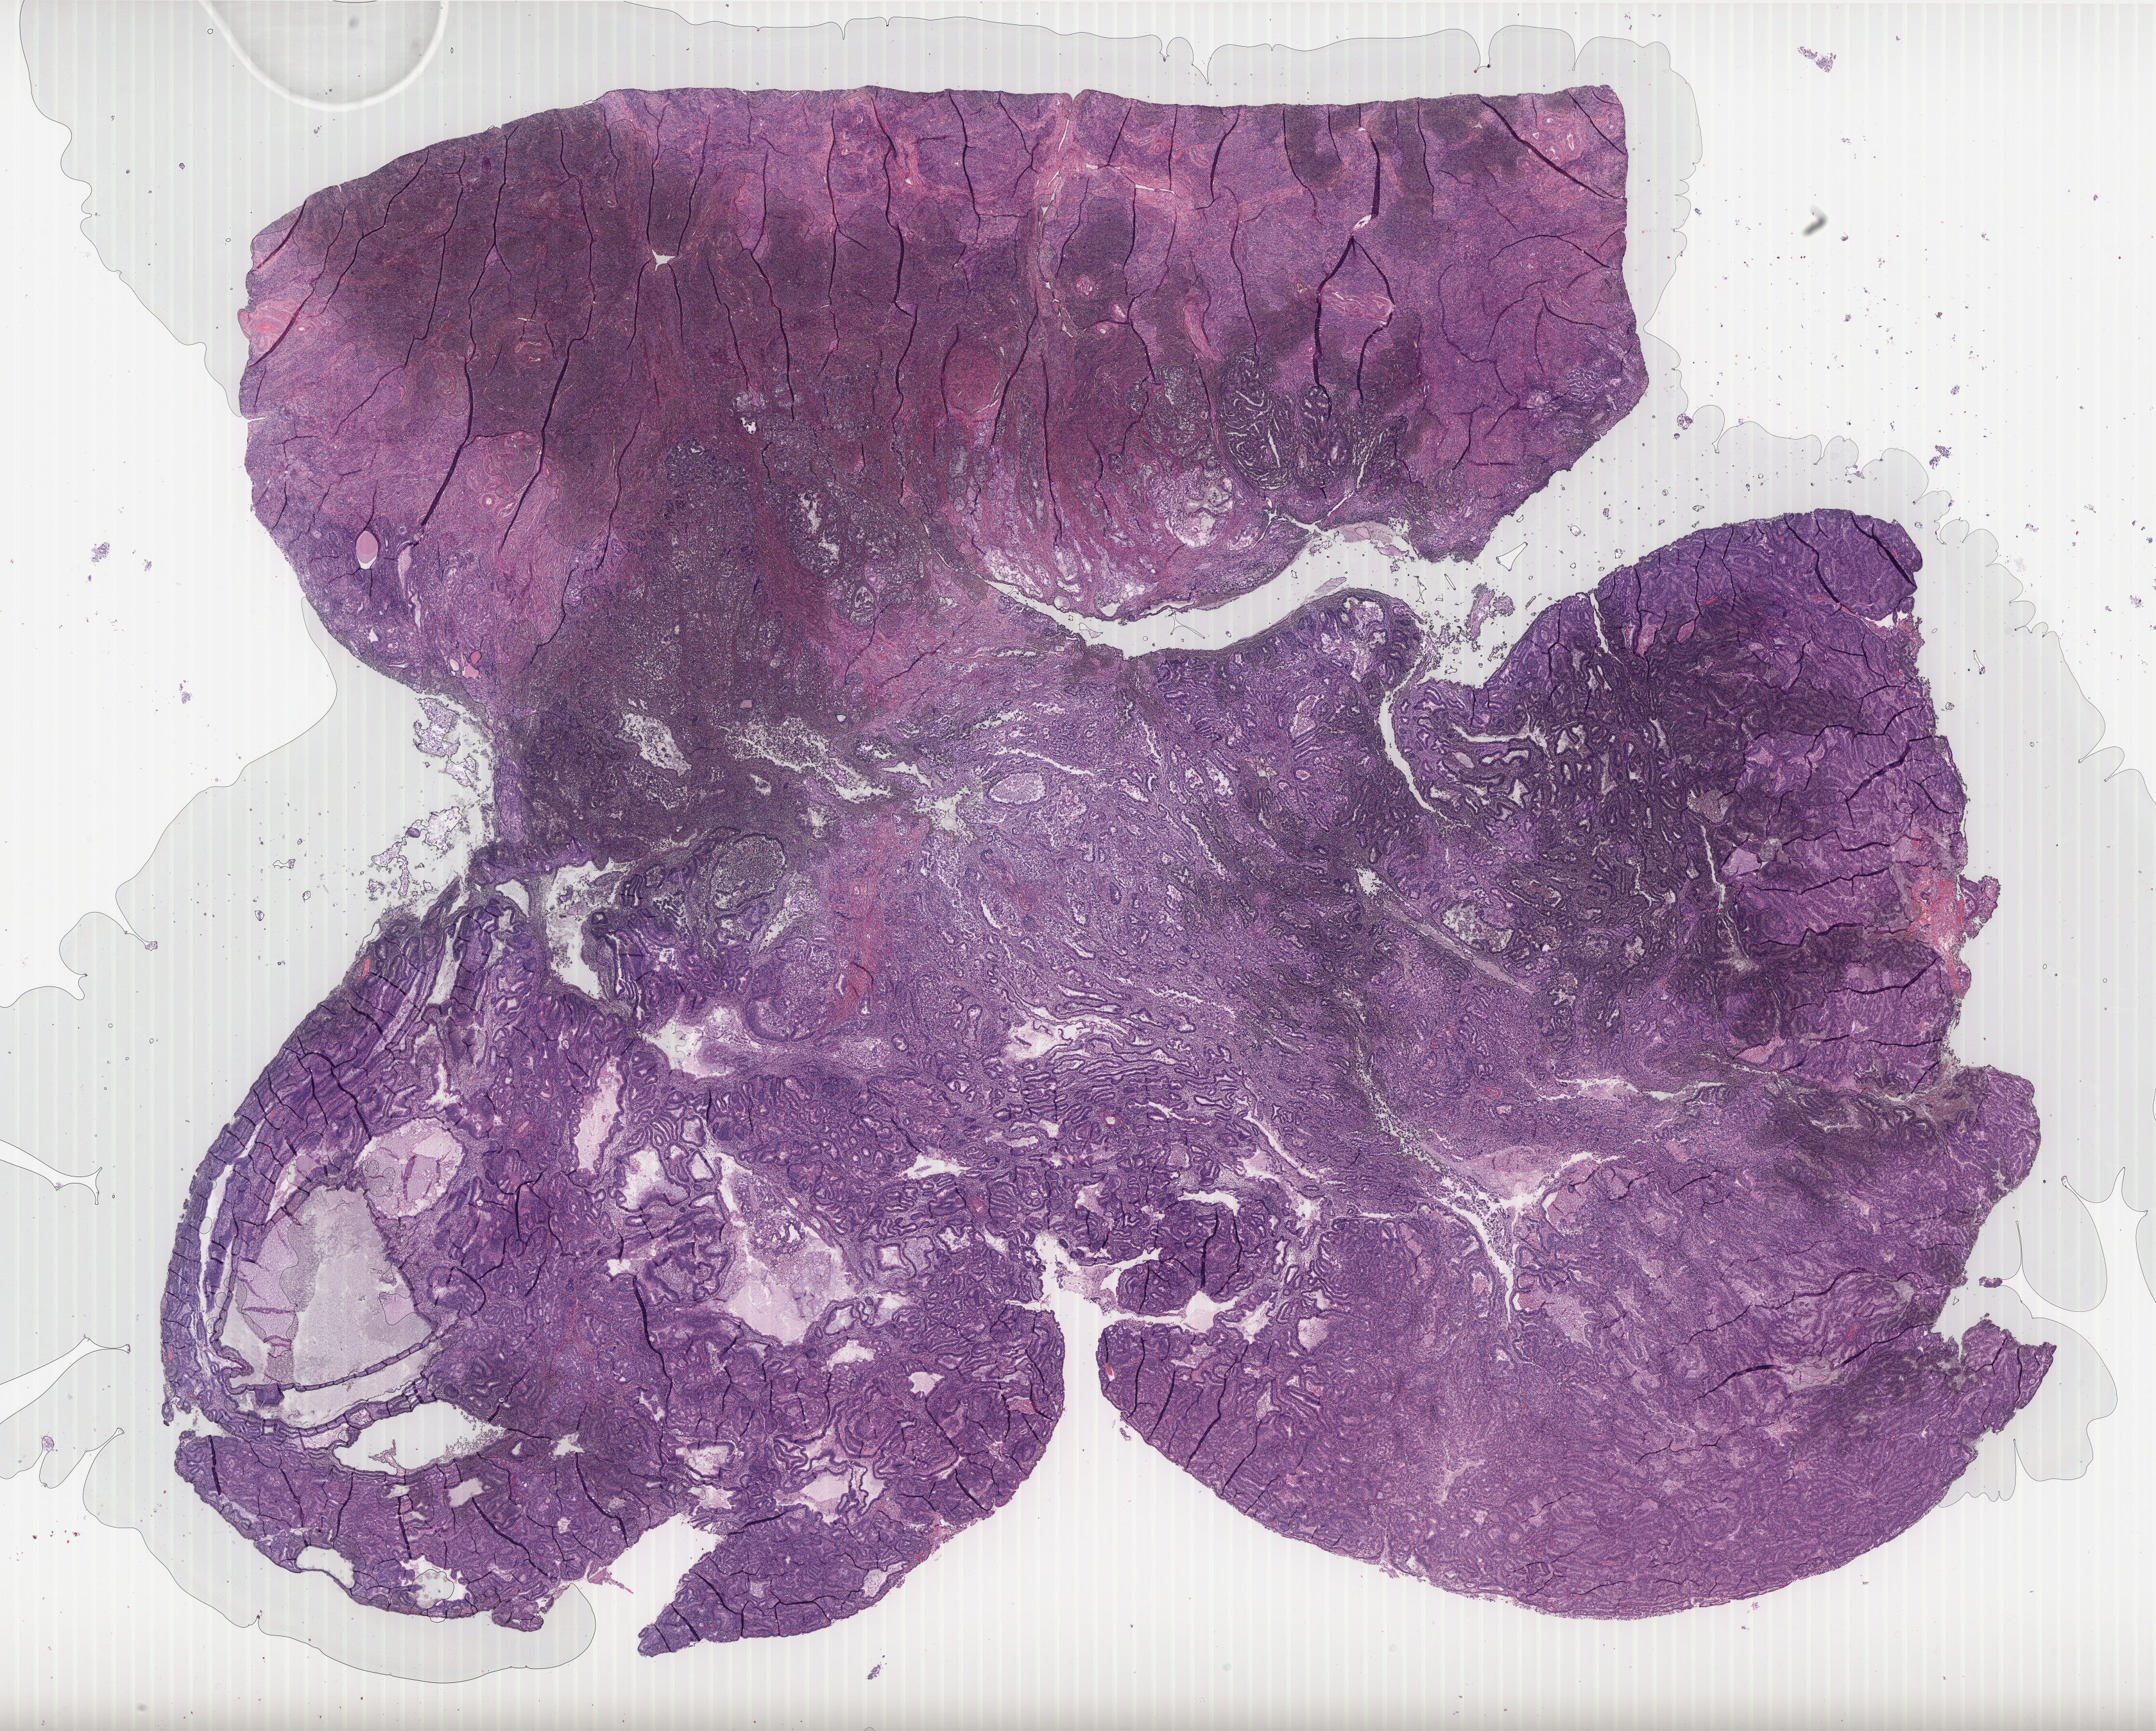
Hematoxylin and eosin (H&E) stained whole-slide image, whole scanned area (about 26.9 x 21.6 mm, from a 40x scan) shown as a low-resolution overview; FFPE section; primary tumour sample from the uterus. Female, age 74 years at initial diagnosis. Histologic grade: G1 (well differentiated).
Diagnosis: Endometrioid adenocarcinoma, NOS (endometrium). FIGO stage: IA.